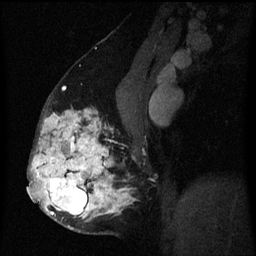
Breast MRI (dynamic contrast-enhanced), one sagittal slice; position 32 of 60 along the scan axis; dynamic contrast-enhanced series, image 2 of 3 at this slice position (ordered by acquisition); 1.5 T; TE 4.2 ms, TR 8 ms; 2 mm slice thickness; 256 × 256 image matrix. Patient: female, 50 years.
Outlined on this slice (semi-automatic segmentation, software-assisted and operator-edited):
- analysis volume of interest (the breast-tissue region the enhancement analysis was run in; not a lesion): bounding box <32,106,132,232> (left, top, right, bottom; pixels)
- tumour enhancement mask (voxels above the 70 % enhancement threshold inside the analysis volume of interest): <32,109,130,227>